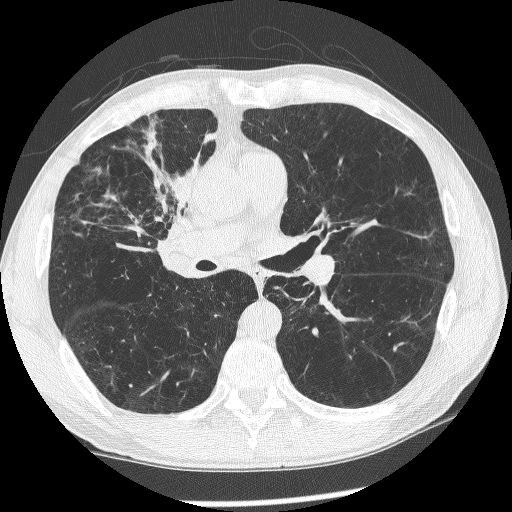
Chest CT (low-dose screening protocol), one axial image; first (baseline) screen; lung window (W 1500 / L -600 HU); lung (sharp) reconstruction kernel (BONE); slice 136 of 266 in the series; 512 × 512 image matrix. Male, age 60 years at enrolment. Current smoker at enrolment.
Expert-annotated lung lesion, box from (x=146, y=177) to (x=216, y=271) px. Screening reader's record for this exam (one nodule recorded; not confirmed to be the boxed lesion): non-calcified nodule or mass ≥4 mm, right upper lobe, 12 × 8 mm, spiculated (stellate) margins, mixed attenuation. Official screen result: positive, change unspecified: nodule(s) >= 4 mm or enlarging nodule(s), mass(es), or other non-specific abnormalities suspicious for lung cancer. Lung cancer was diagnosed 208 days after this screen: squamous cell carcinoma, NOS, right upper lobe, right middle lobe, right main stem bronchus, poorly differentiated (G3), stage IV (AJCC 6th edition).